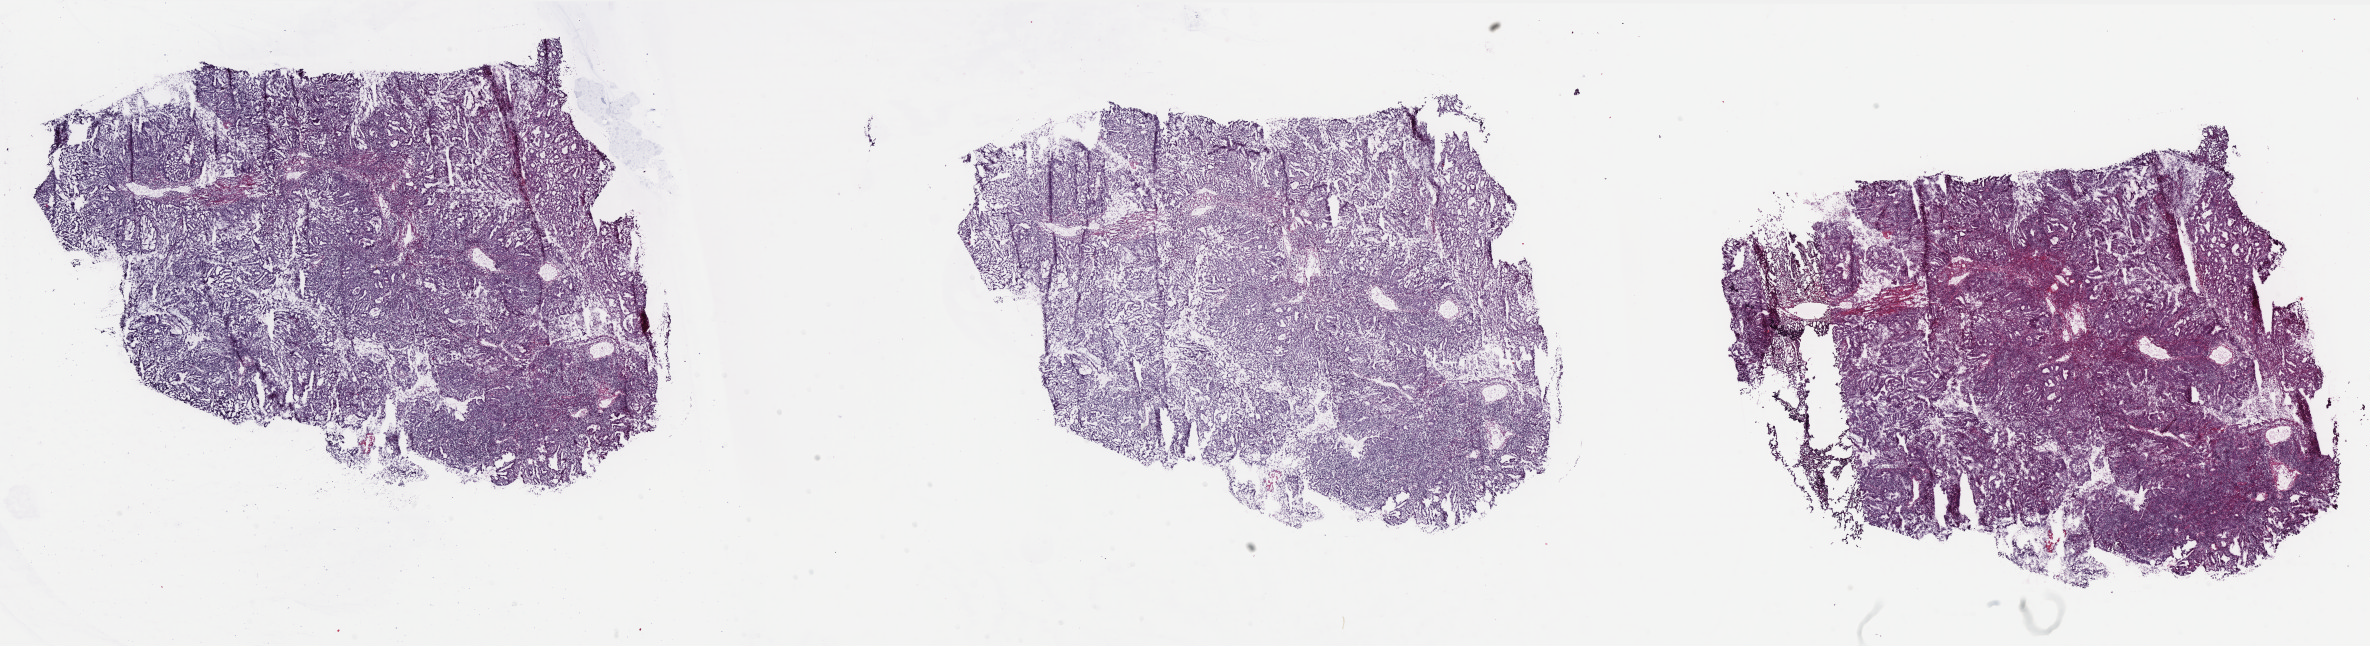
Digitized H&E tissue section (whole slide), shown as a low-resolution overview of the whole scanned area (about 38.0 x 10.4 mm); frozen section; uterus, primary tumour sample. Female patient; age at initial diagnosis 60 years. Histologic grade: G1 (well differentiated). Pathologist review of this section (percent, as recorded): tumour cells 55%, tumour nuclei 20%, normal cells 5%, stromal cells 35%, necrosis 5%. Infiltration values recorded for this section: lymphocyte infiltration 70%, monocyte infiltration 0%, neutrophil infiltration 0%.
• pathologic diagnosis: Endometrioid adenocarcinoma, NOS (endometrium)
• FIGO stage: IIIA
• lymph nodes positive (case pathology): 0 of 4 examined